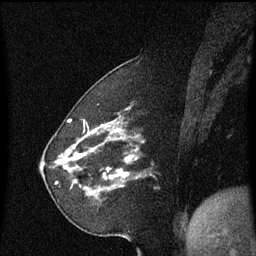
Breast MRI (dynamic contrast-enhanced), one sagittal slice. Slice 18 of 60 in the series (ordered by position). Dynamic contrast-enhanced series, image 2 of 3 at this slice position (ordered by acquisition). 1.5 T. TE 4.2 ms, TR 8.4 ms. 256 × 256 image matrix, field of view 200 × 200 mm. Female patient, age 60 years. Case-level facts recorded for this patient, not image findings: setting: breast cancer imaged before/during neoadjuvant chemotherapy; receptor status: triple-negative.
Outlined on this slice (semi-automatic segmentation, software-assisted and operator-edited):
- analysis volume of interest (the breast-tissue region the enhancement analysis was run in; not a lesion): bounding box (x1, y1, x2, y2) in pixels: (68, 142, 144, 201)
- tumour enhancement mask (voxels above the 70 % enhancement threshold inside the analysis volume of interest): (70, 156, 133, 179)